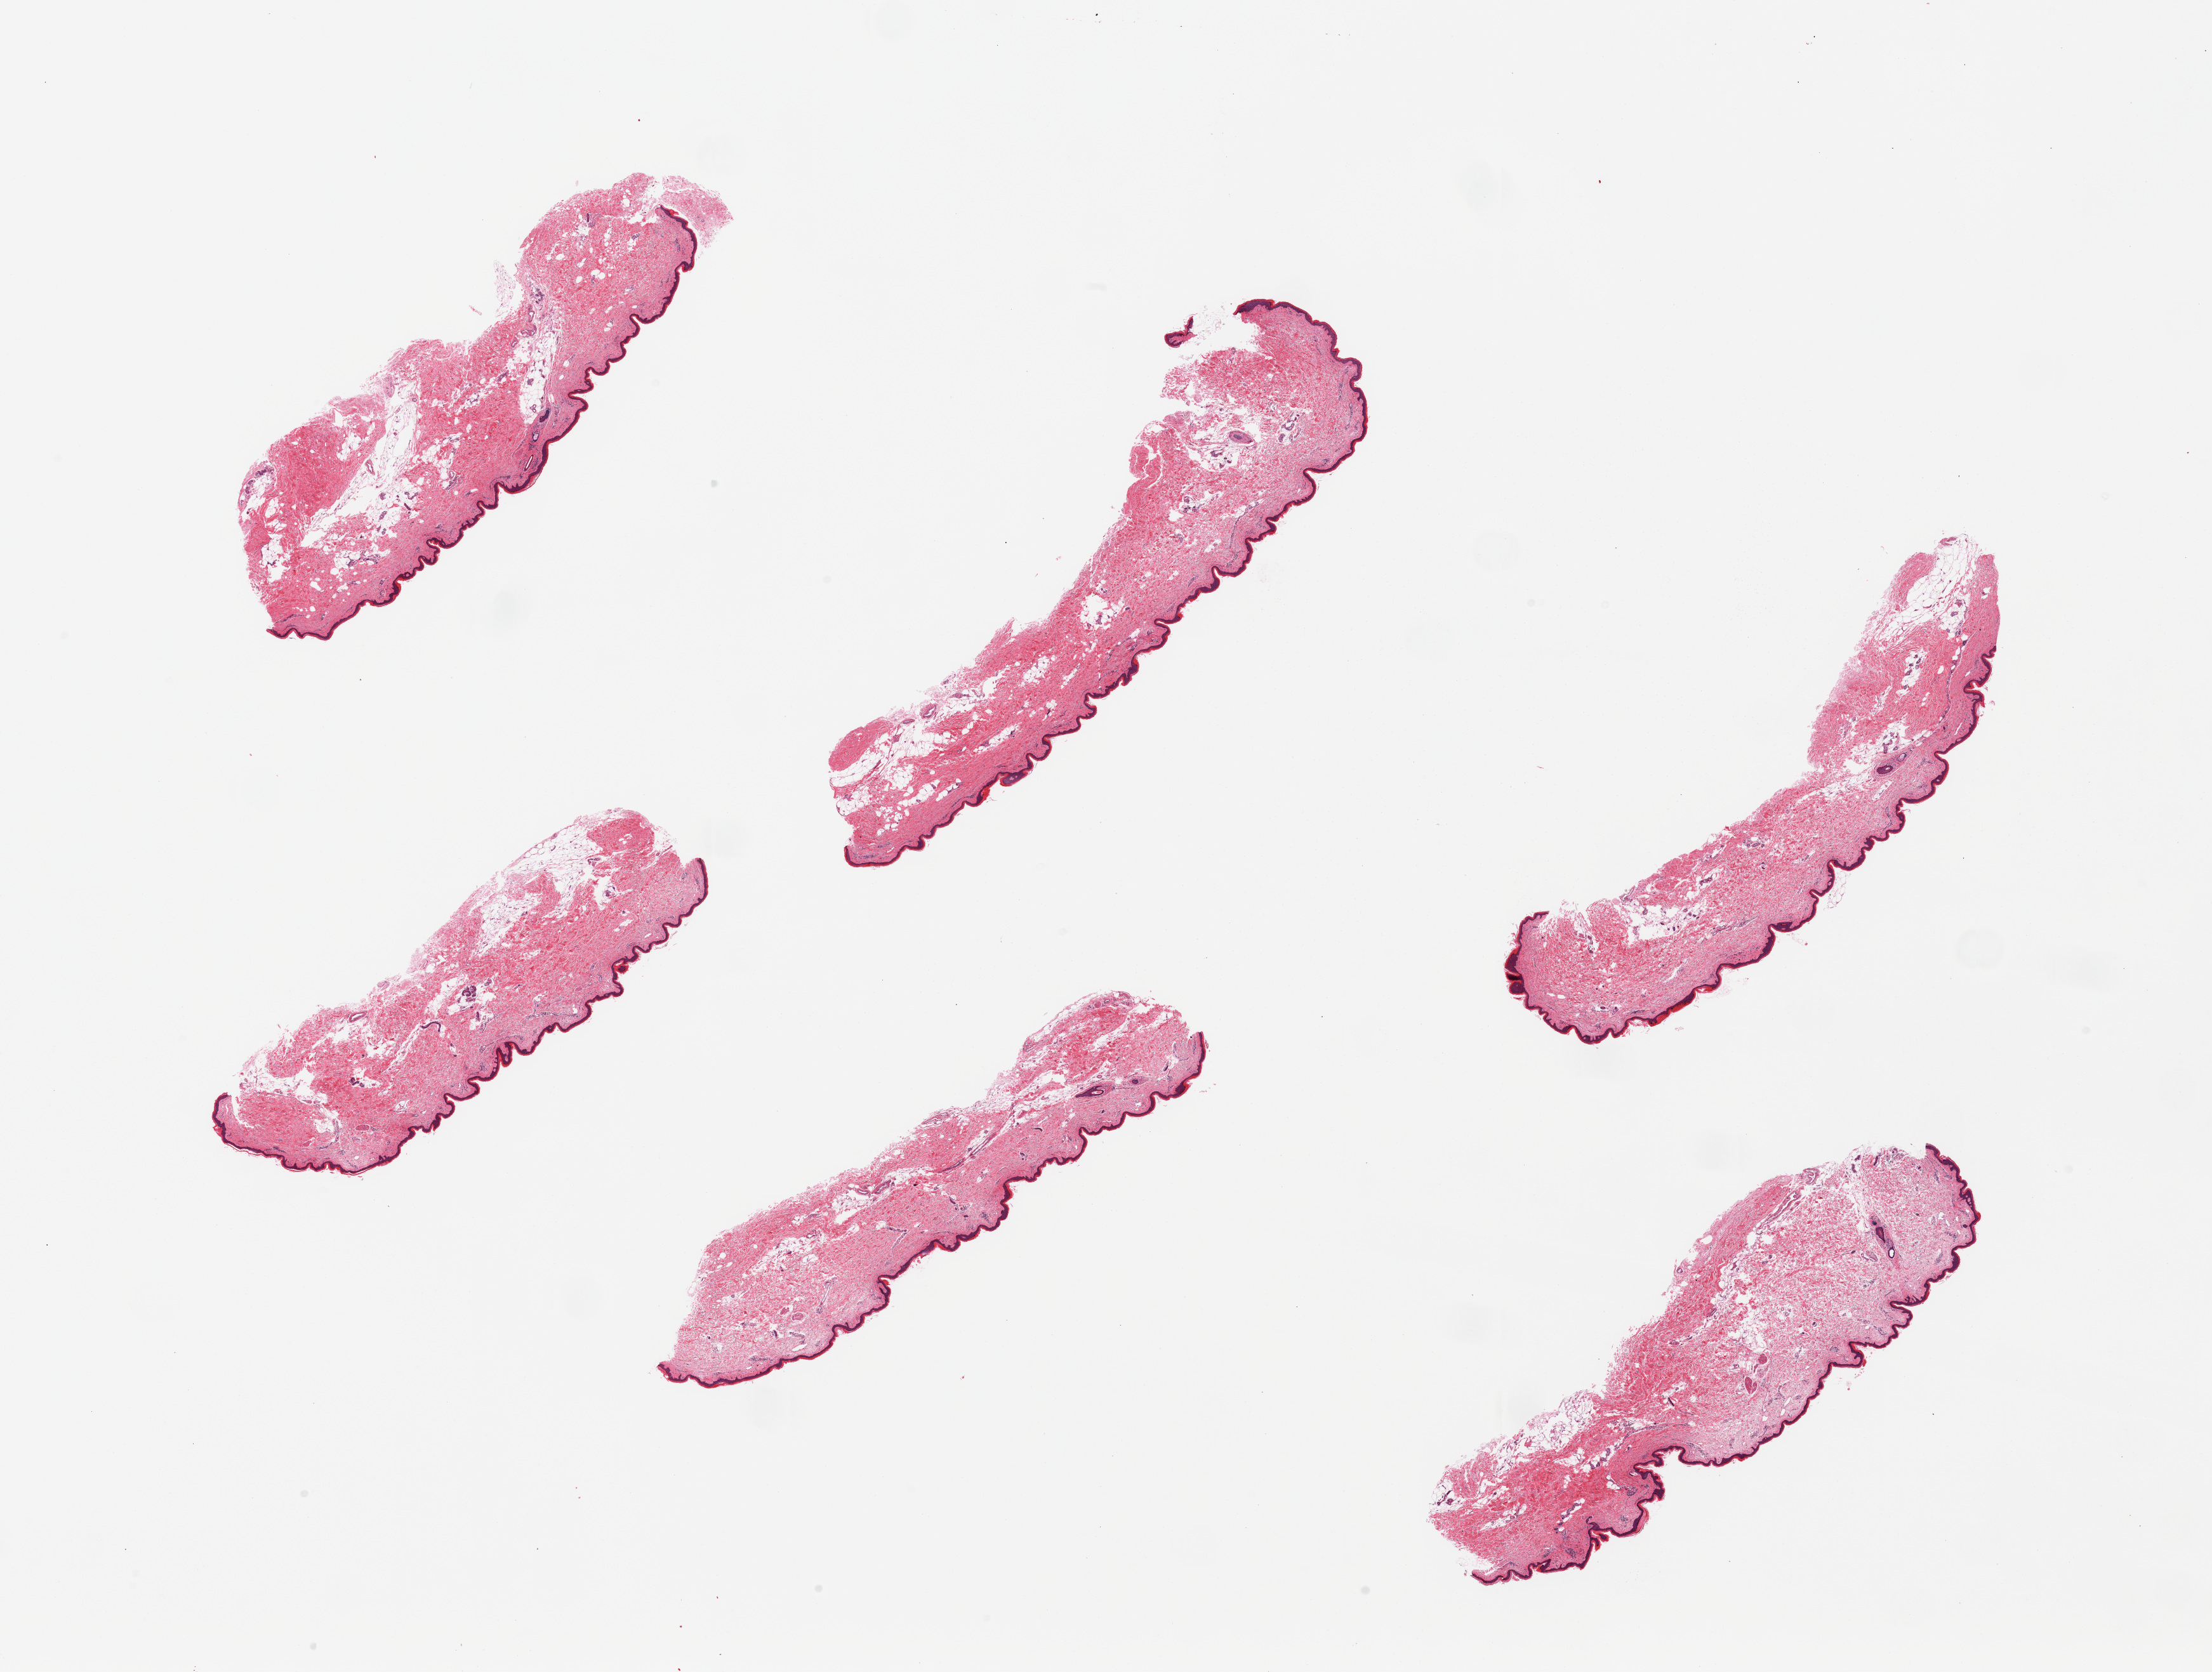
Whole-slide image, hematoxylin and eosin (H&E) stain — low-resolution overview of the scanned area, about 27.6 x 20.8 mm (from a 20x scan), PAXgene-fixed, paraffin-embedded tissue, sampled site (target tissue): skin of lower leg, donor tissue sample.
Reviewer comment on this tissue sample: 6 pieces, include up to 10% internal and attached fat, squamous epithelium measures ~31 microns.